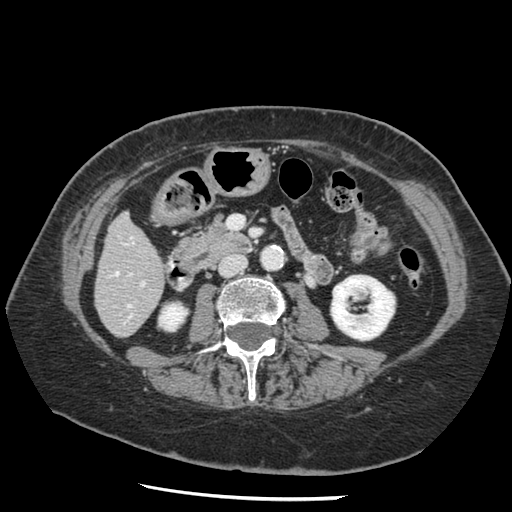
Contrast-enhanced abdominal CT, one axial slice; slice 41 of 148 in the series (ordered by position); reconstruction kernel STANDARD; 120 kVp; intravenous contrast given; soft-tissue window (W 400 / L 40 HU); 2.5 mm slice thickness; 512 × 512 image matrix, field of view 330 × 330 mm. Female patient, age 85 years. From the clinical record (not read from this slice): diagnosis: colorectal cancer liver metastases, imaged before liver resection; multiple liver metastases: no.
Annotated regions visible in this slice (expert manual segmentation):
- hepatic veins: bounding box [x1, y1, x2, y2] px = [115, 272, 131, 308]
- liver: [96, 215, 165, 337]
- planned liver remnant (the part of the liver to remain after resection): [96, 215, 165, 334]